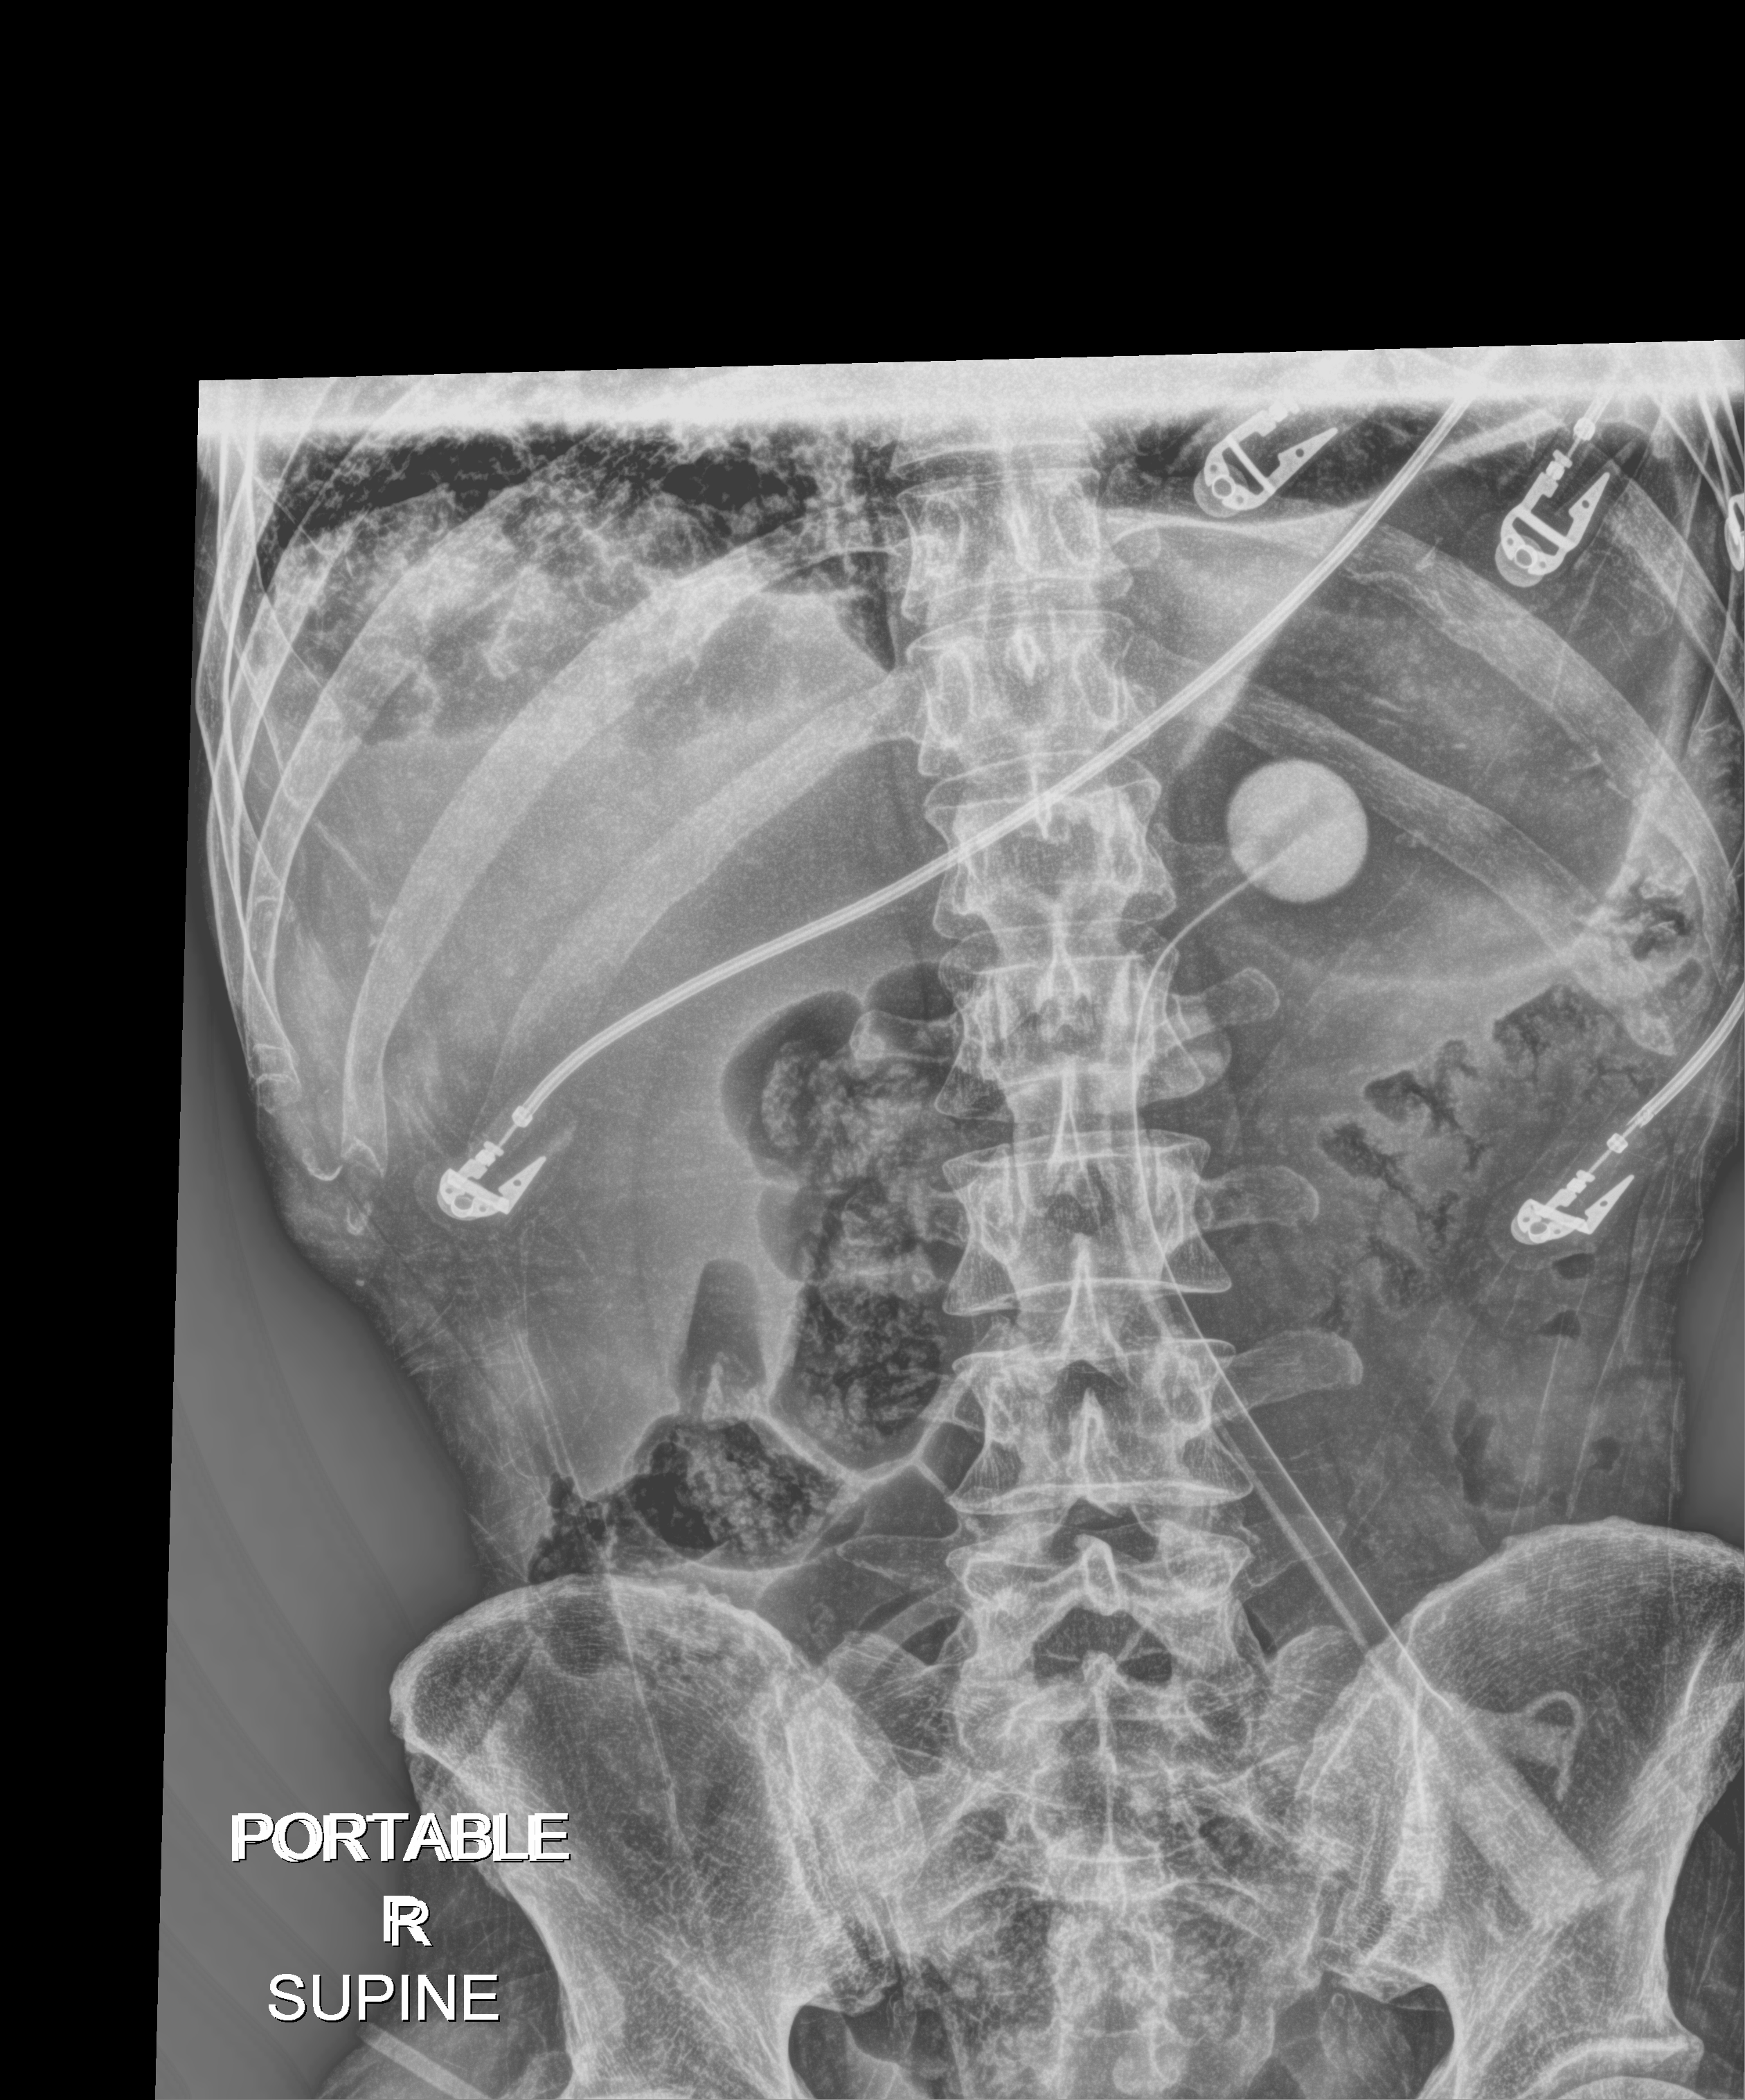
Bedside abdomen radiograph (digital radiography); anteroposterior (AP) projection. Male patient hospitalised with COVID-19, age 18–59 years.
From the hospital-stay record, not from the radiograph (when in the stay this image was taken is not recorded): chronic kidney disease (admission record): no; admitted to intensive care during this hospital stay: yes; diabetes (admission record): yes.